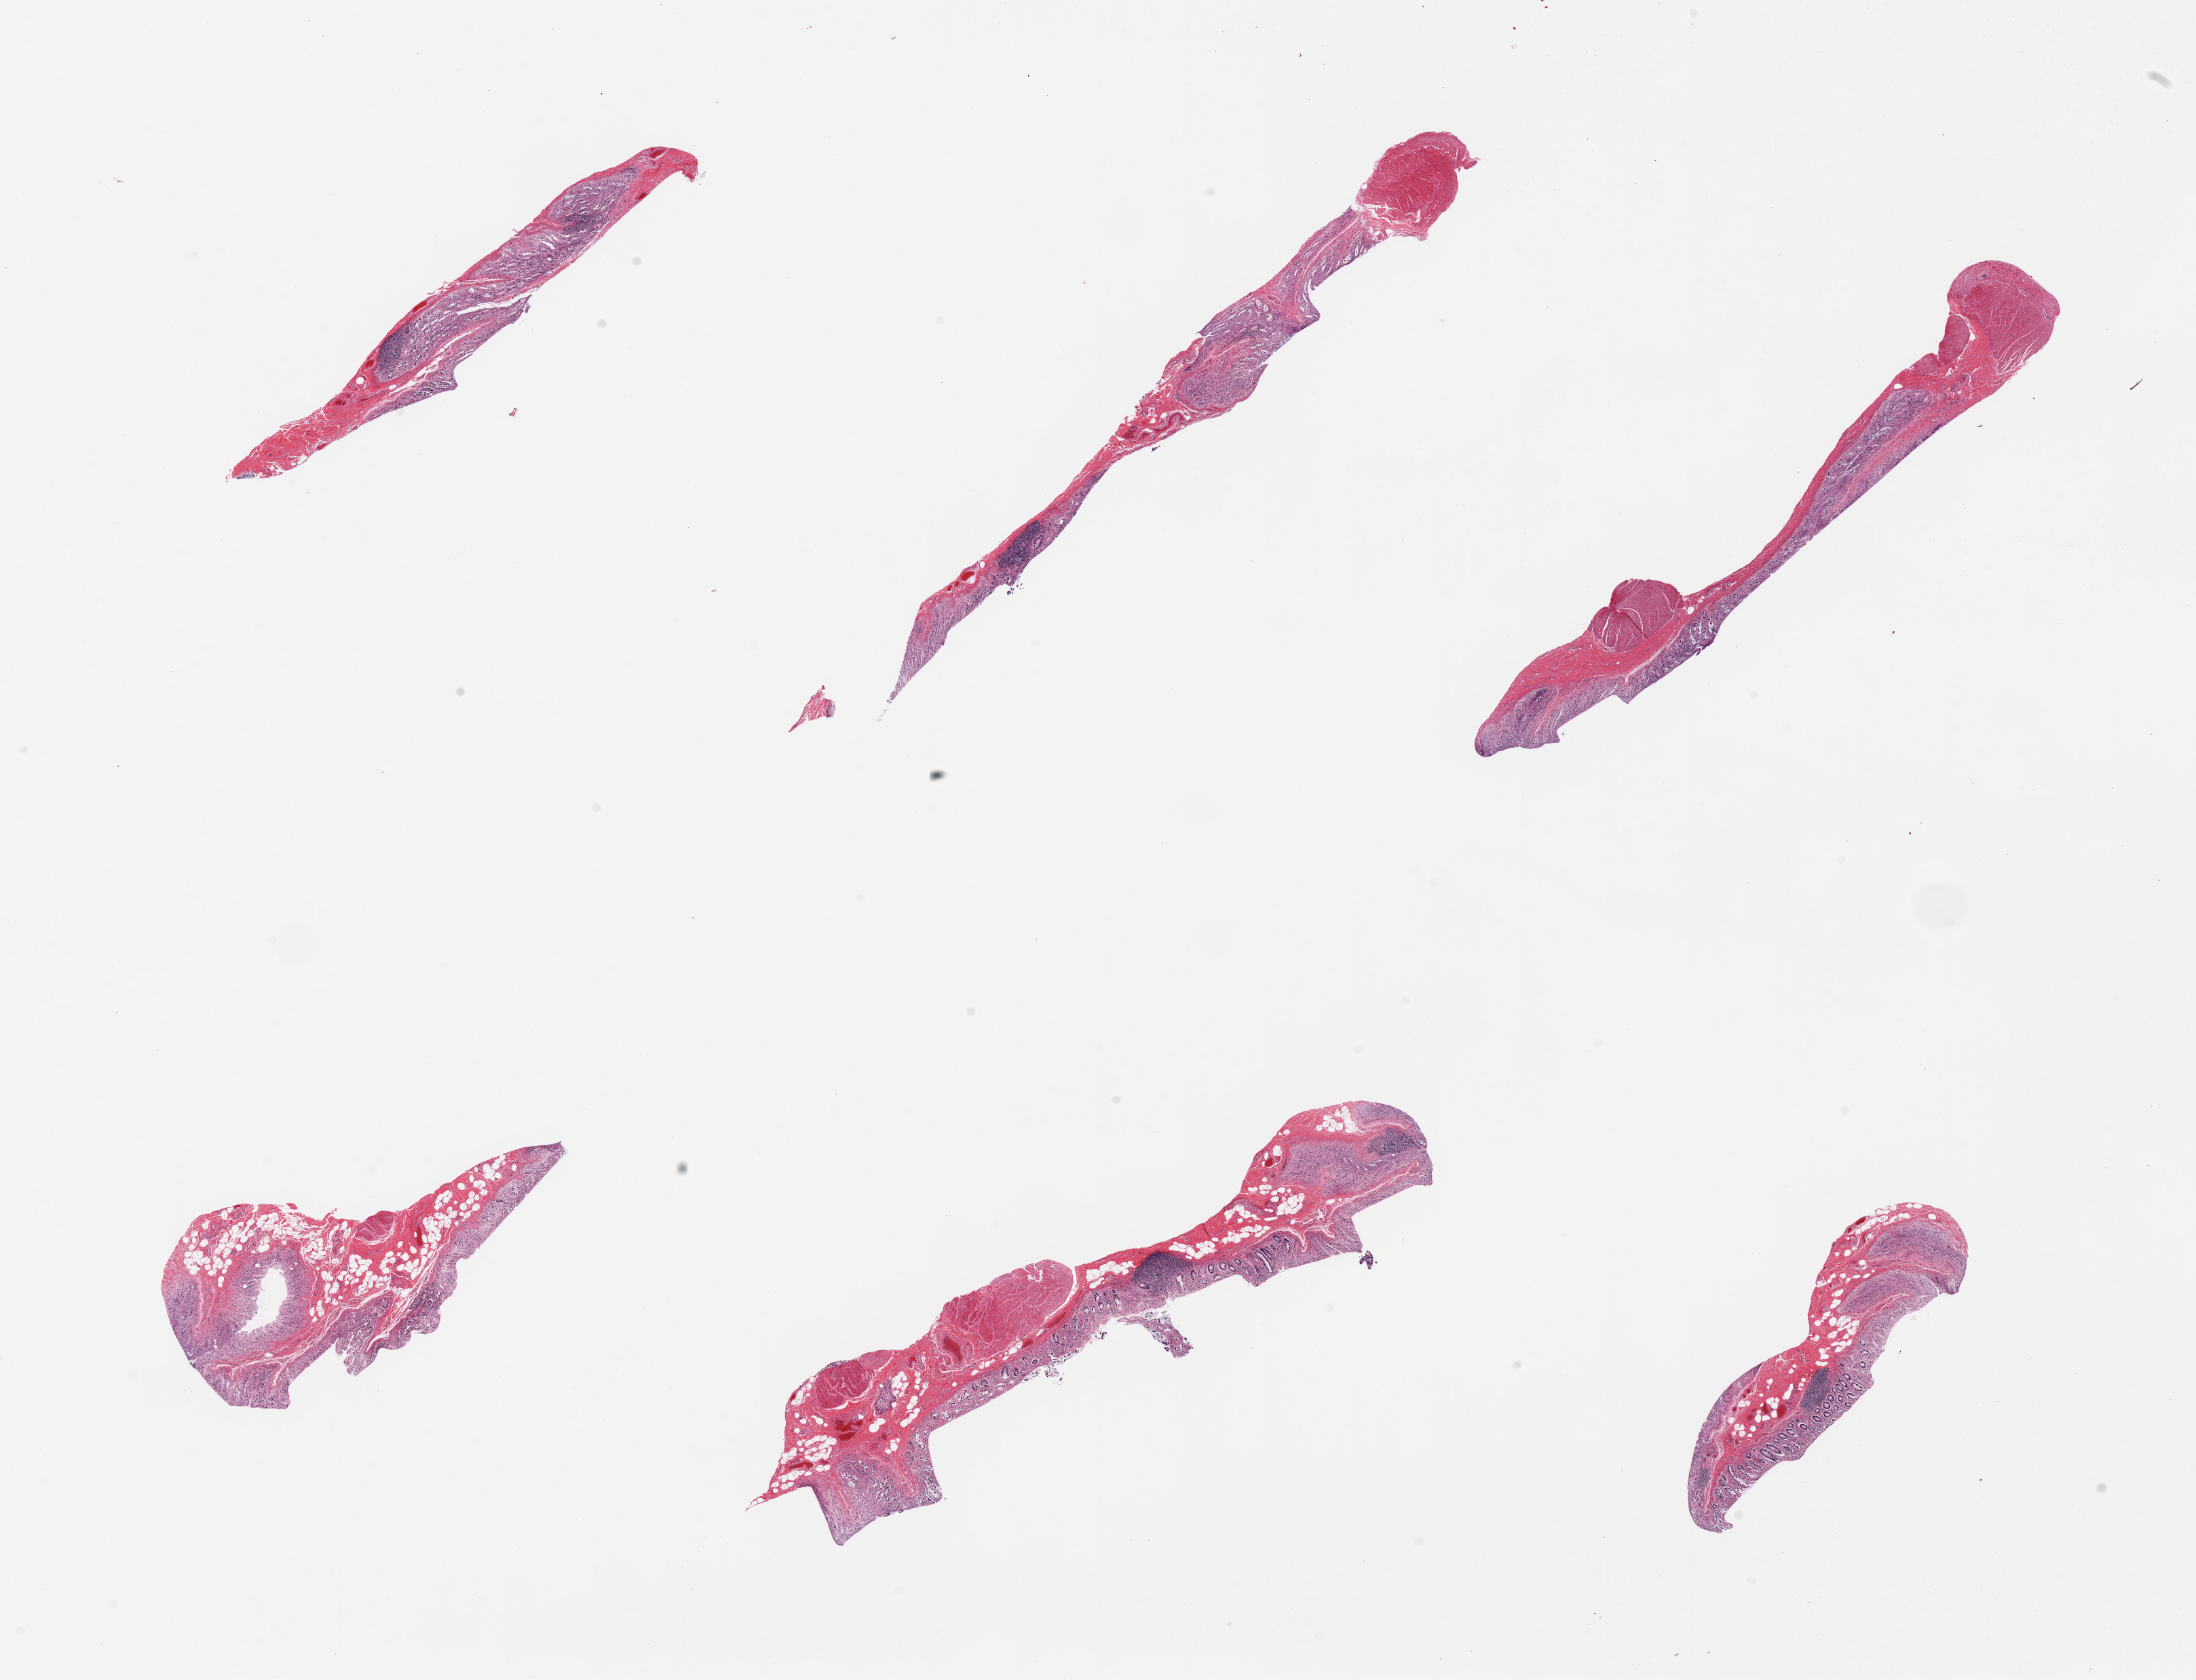
Digitized hematoxylin and eosin (H&E)-stained section, brightfield — a low-resolution overview of the entire scanned area, about 25.6 x 19.6 mm (slide scanned at 20x). PAXgene-fixed, paraffin-embedded tissue. Section of transverse colon (target tissue). Donor tissue sample. Female donor.
- reviewer comment on this tissue sample: 6 pieces, severely autolyzed mucosa, some muscularis (not target)